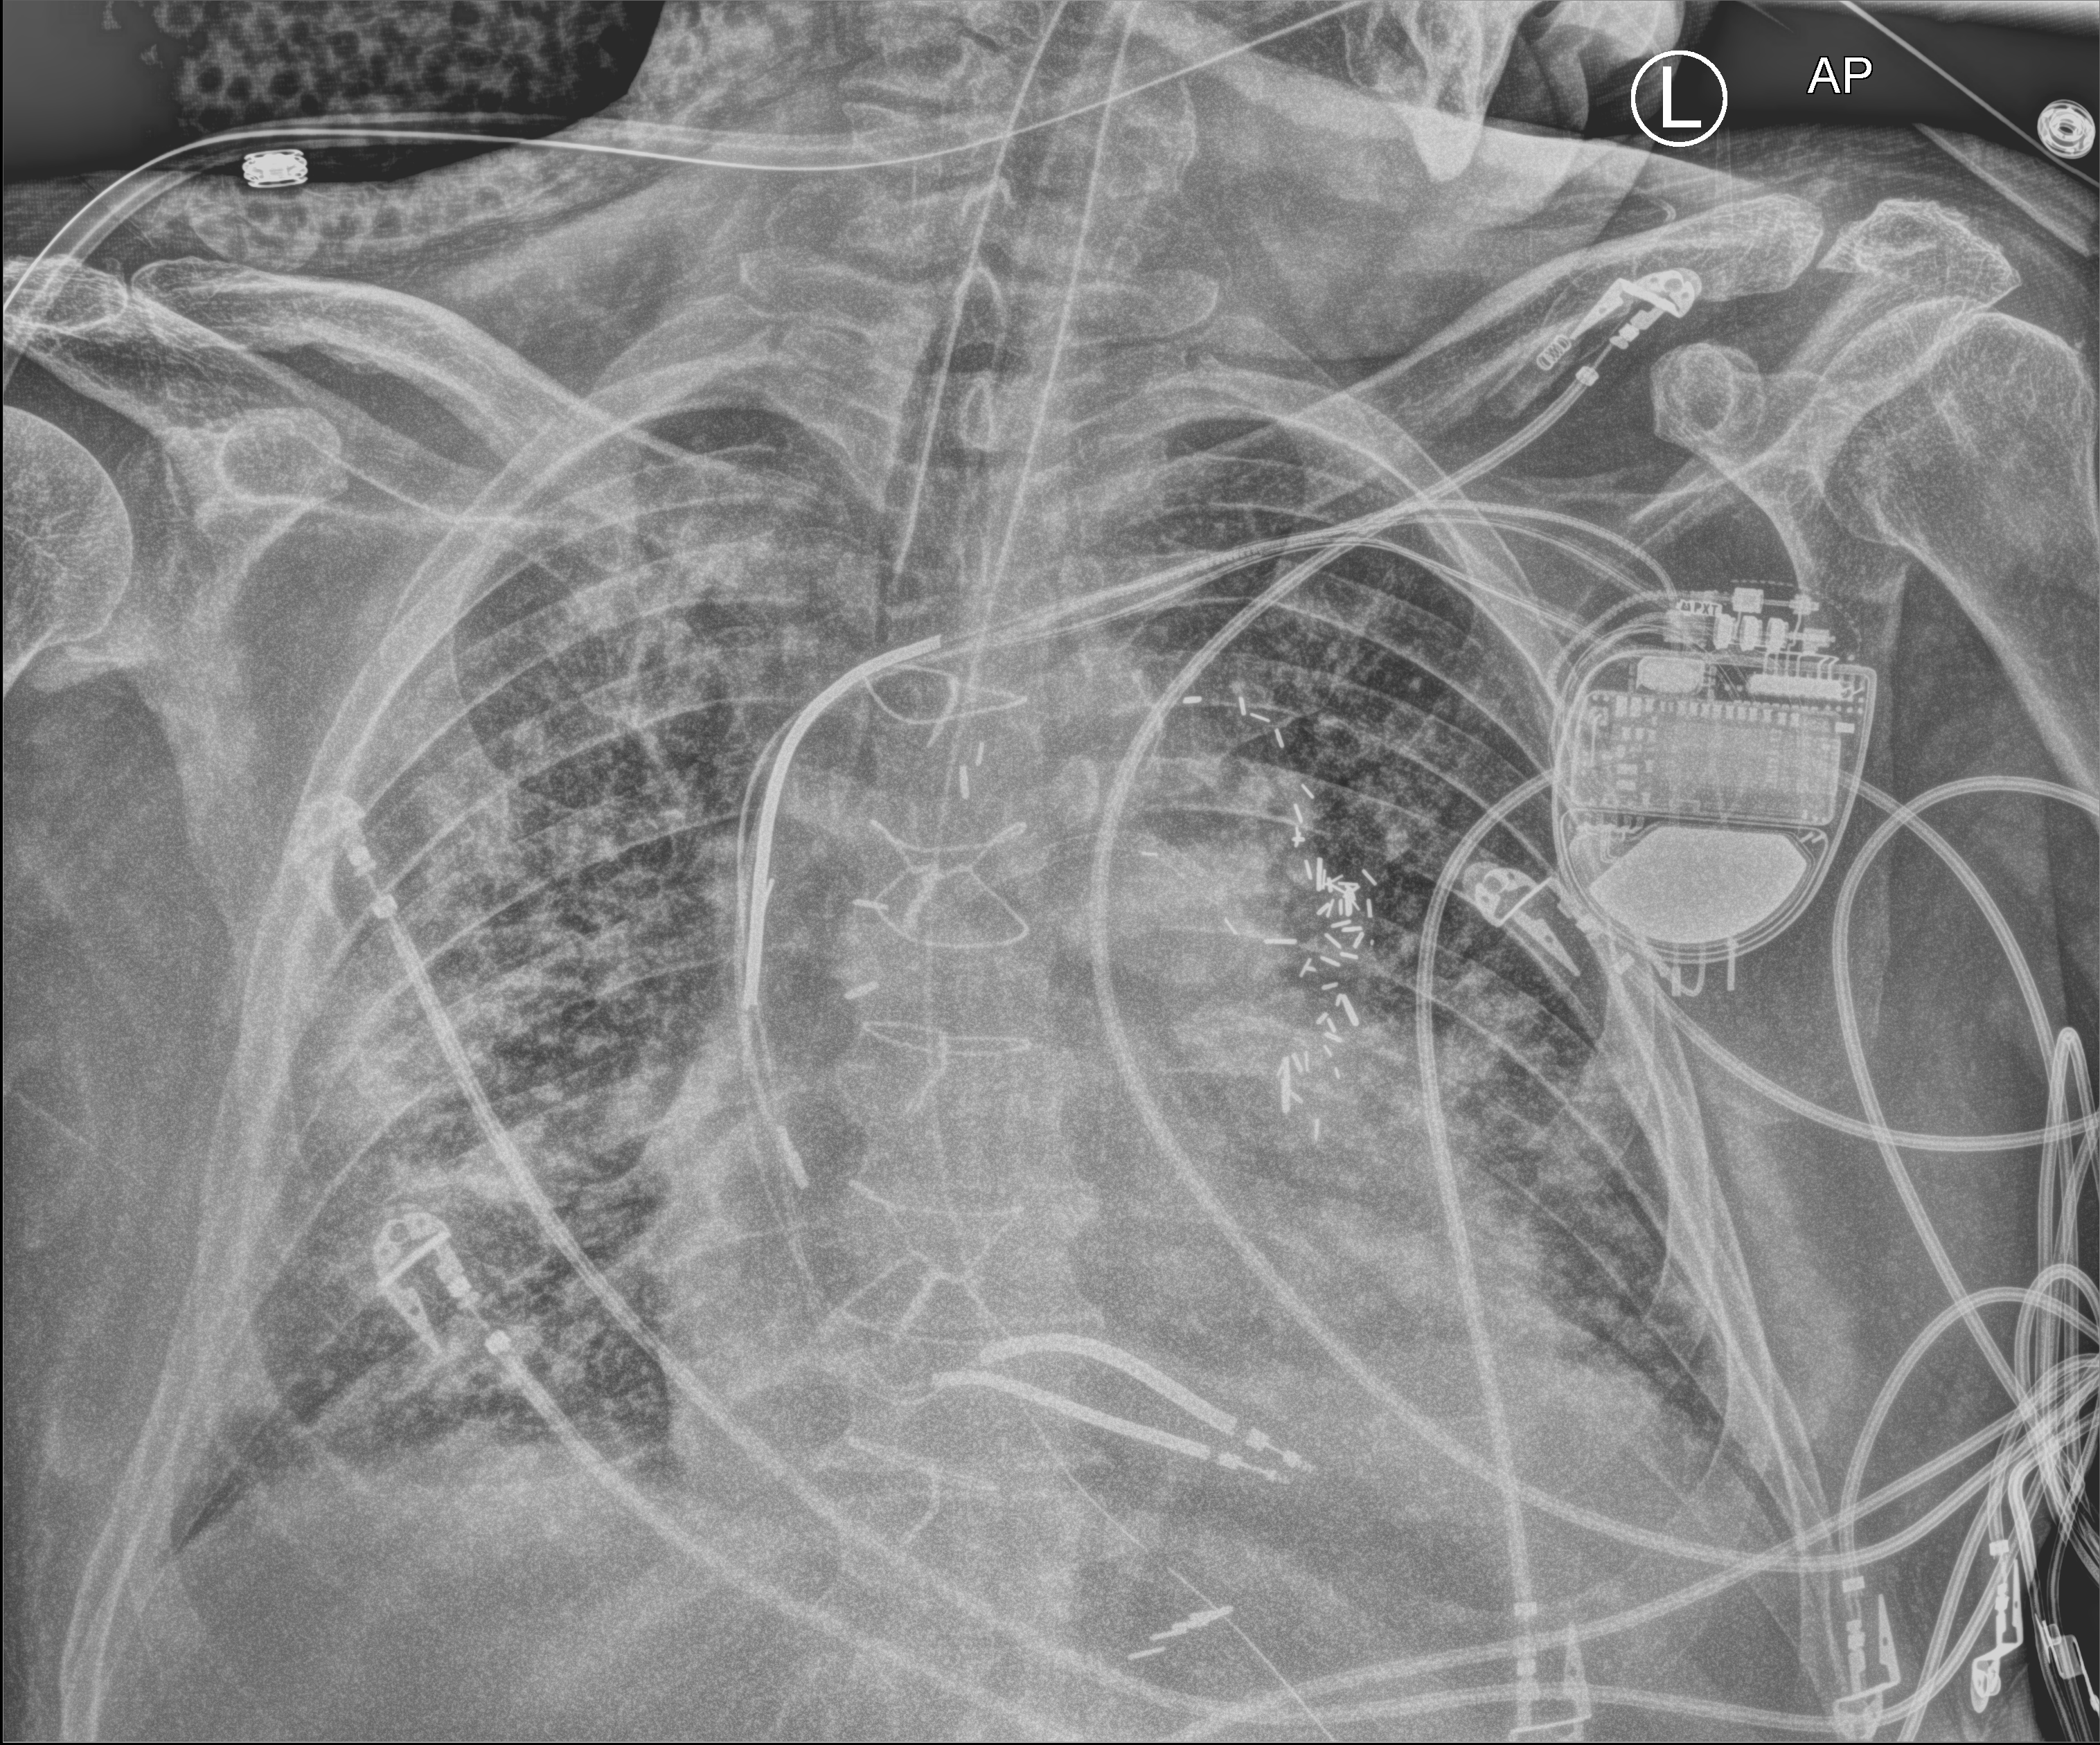
Bedside chest radiograph (computed radiography), anteroposterior (AP) projection. Male patient hospitalised with COVID-19, age 60–74 years.
From the hospital-stay record, not from the radiograph (when in the stay this image was taken is not recorded): admitted to intensive care during this hospital stay: yes.